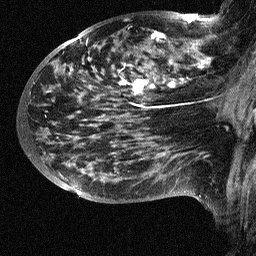
Breast MRI (dynamic contrast-enhanced), one sagittal slice. Slice 37 of 64 in the series (ordered by position). Dynamic contrast-enhanced study with each time point stored as its own series, time point 2 of 3 at this slice position (early post-contrast, ordered by acquisition time). 1.5 T. TE 4.5 ms, TR 11 ms. 256 × 256 image matrix, field of view 200 × 200 mm. Female patient, age 38 years. From the clinical record (not read from this slice): setting: breast cancer imaged before/during neoadjuvant chemotherapy; receptor status: HR-positive, HER2-negative.
Annotated regions visible in this slice (semi-automatically segmented with operator editing):
- analysis volume of interest (the breast-tissue region the enhancement analysis was run in; not a lesion): box from (x=88, y=18) to (x=252, y=126) px
- tumour enhancement mask (voxels above the 90 % enhancement threshold inside the analysis volume of interest): (x=120, y=18)–(x=206, y=107)